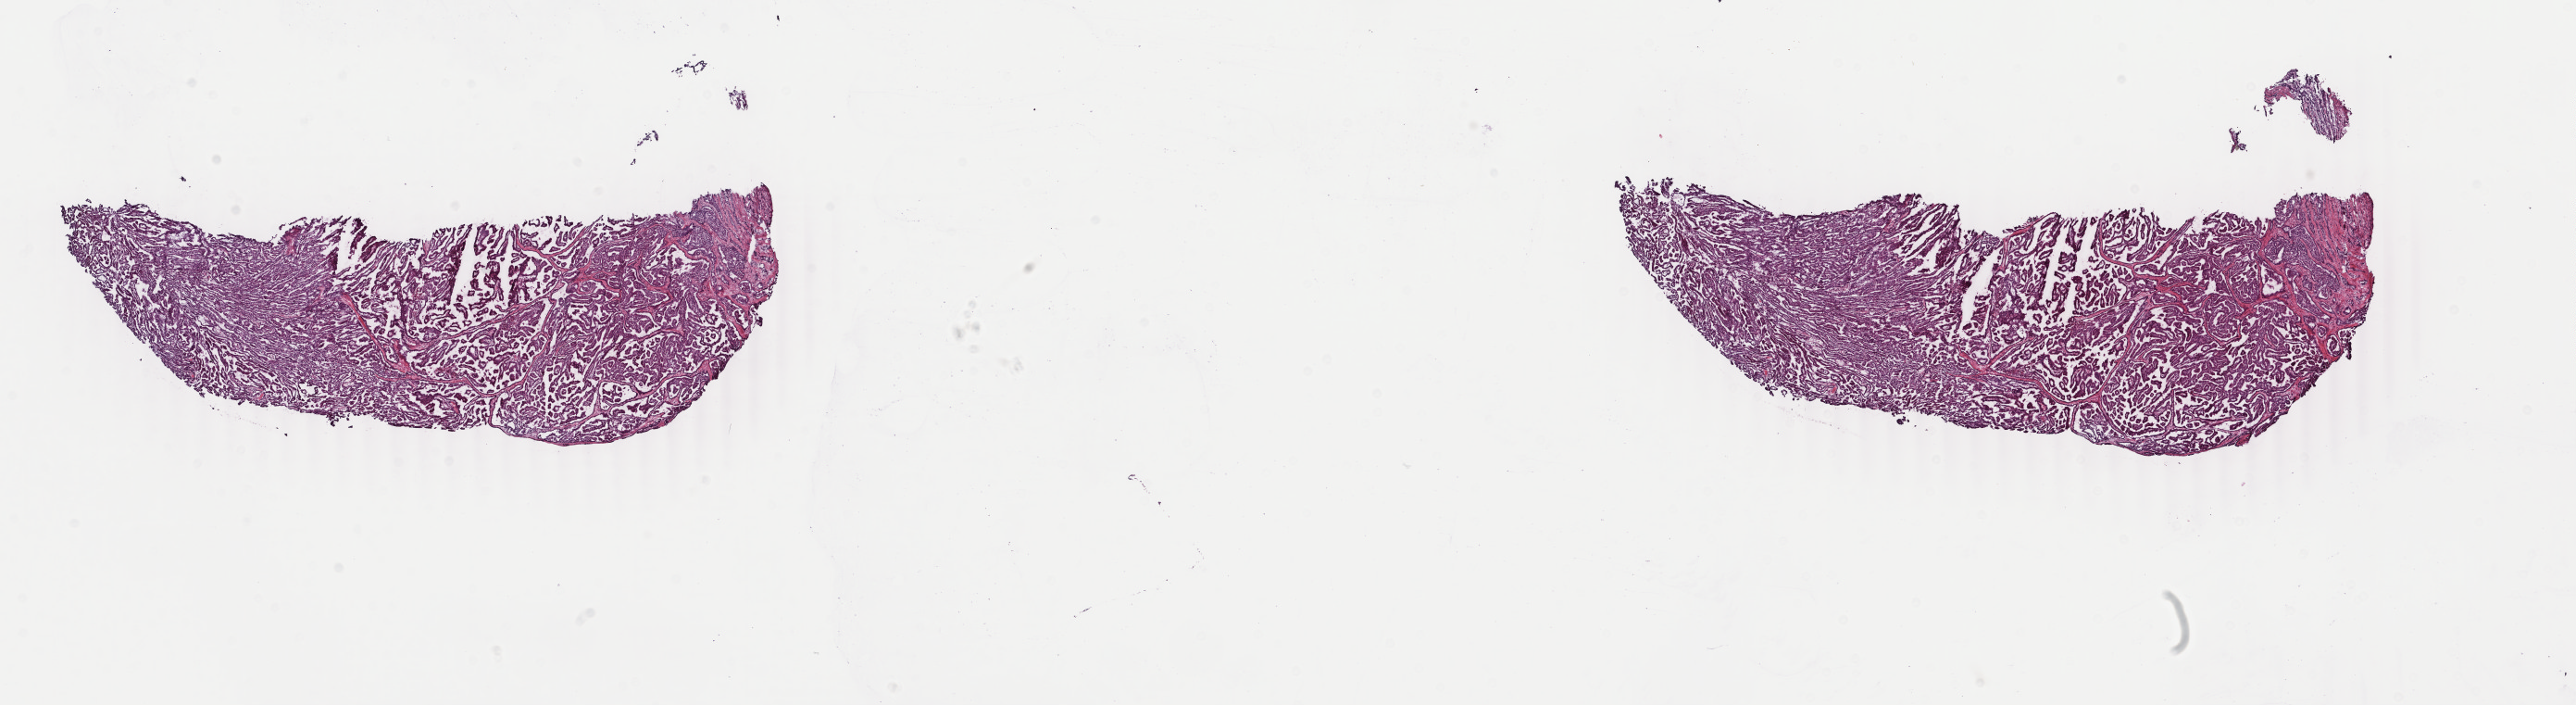
H&E whole-slide image, whole scanned area (about 22.1 x 6.1 mm, from a 40x scan) shown as a low-resolution overview. Frozen section from the top of the tissue portion. Sample: primary tumour, kidney. Patient: male, age at initial diagnosis 58 years. Composition of this section per pathologist review: tumour cells 100%, tumour nuclei 80%, normal cells 0%, stromal cells 0%, necrosis 0%. Infiltration values recorded for this section: lymphocyte infiltration 2%, monocyte infiltration 3%, neutrophil infiltration 0%.
Diagnosis: Papillary adenocarcinoma, NOS.